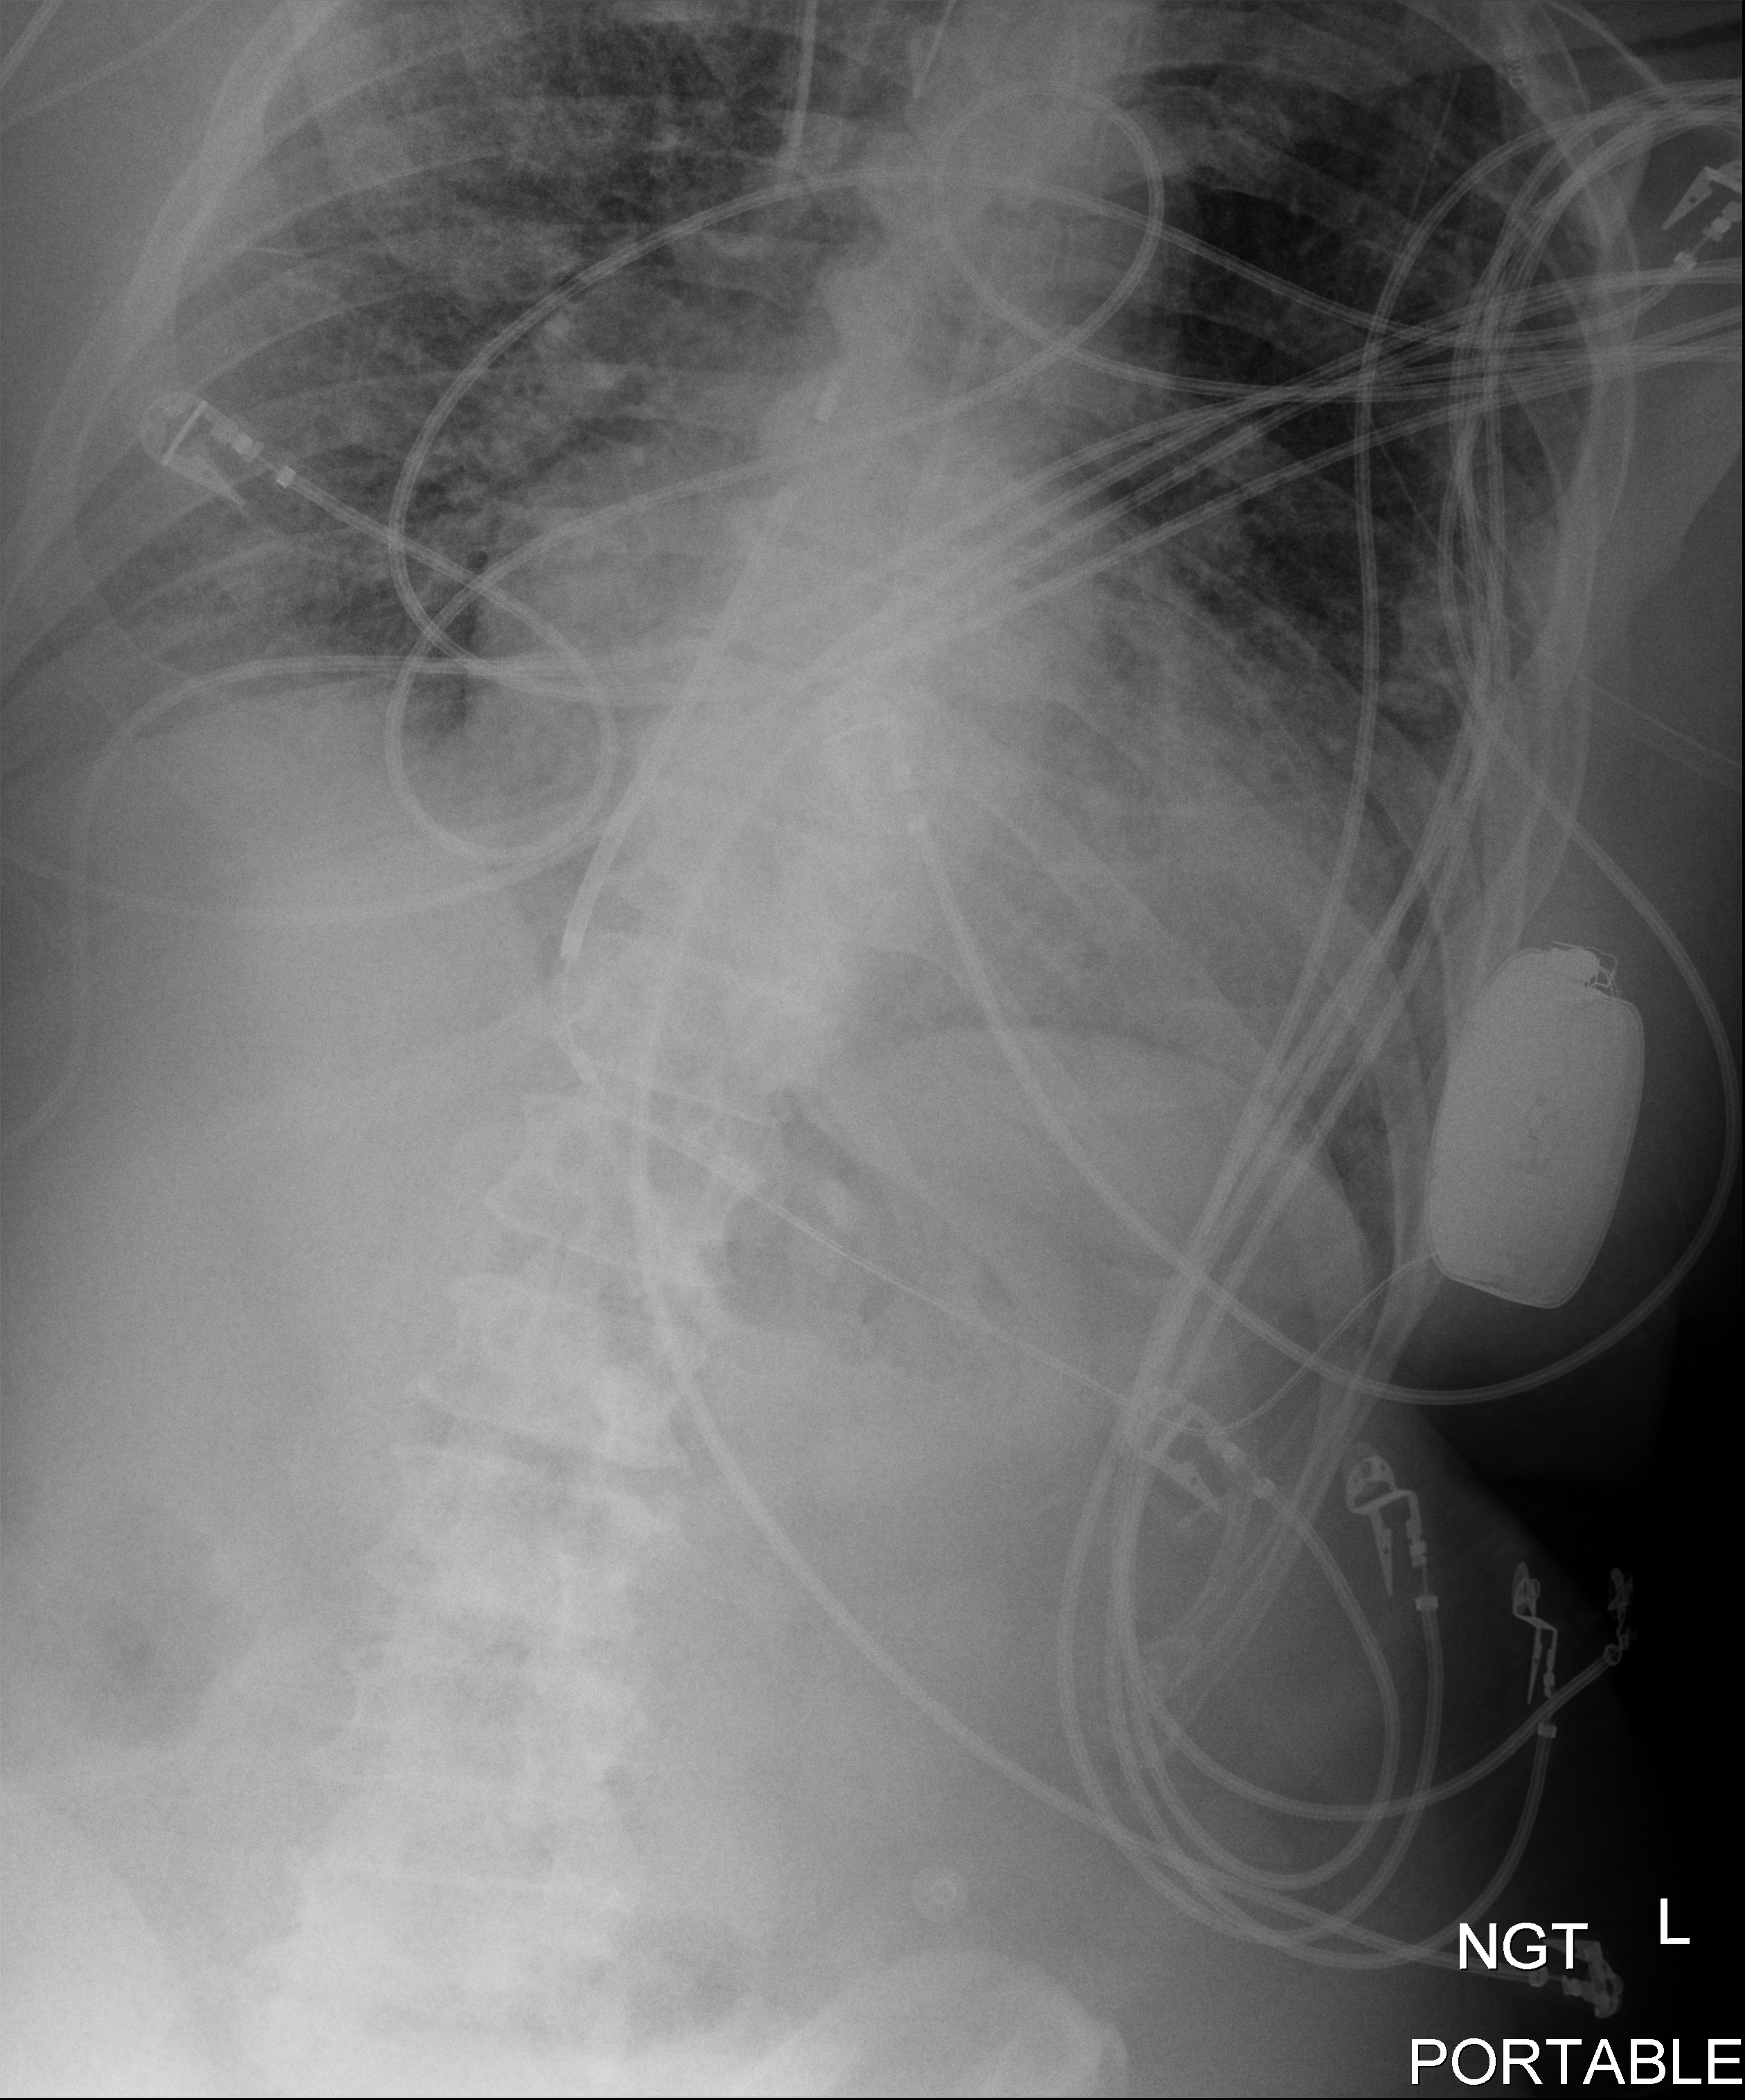
Bedside chest radiograph (digital radiography). Male patient hospitalised with COVID-19, age 60–74 years.
Admission-level facts for this patient (not findings on this image; timing relative to this image not recorded):
- smoking status (admission record): never
- length of hospital stay: 16 days